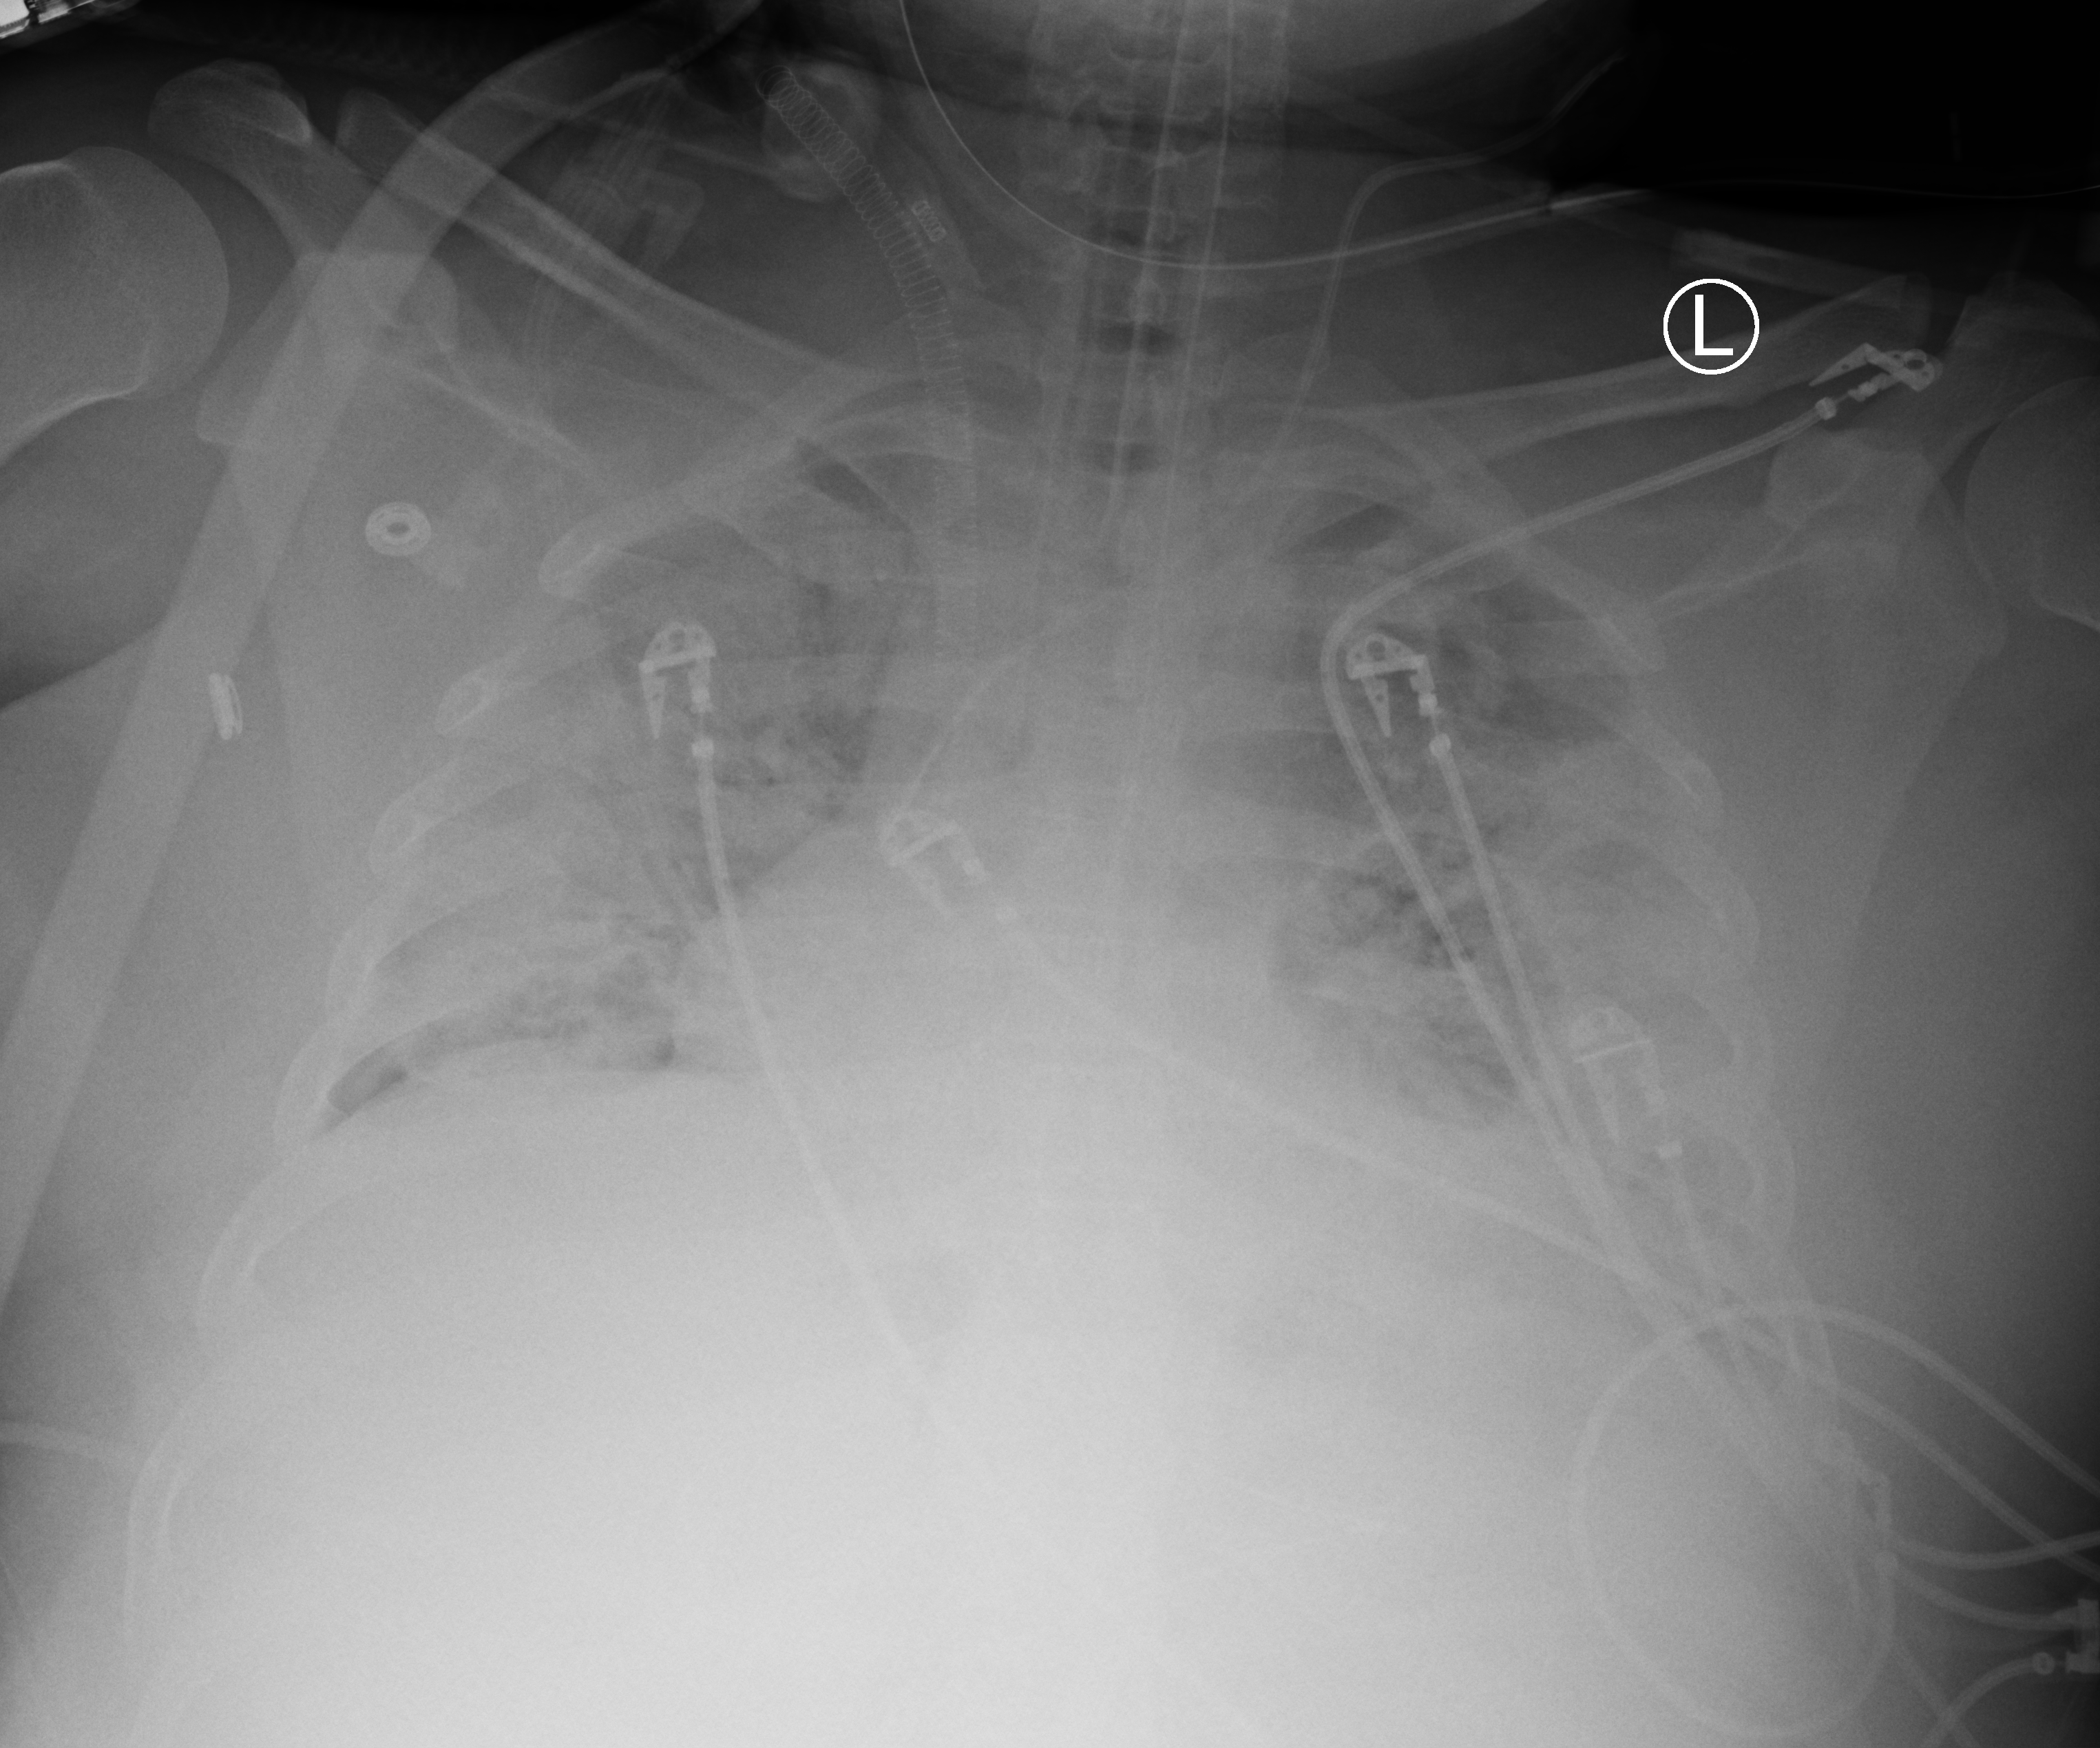
Chest X-ray (portable), anteroposterior (AP) projection. Adult patient hospitalised with COVID-19, age 18–59 years.
Admission-level facts for this patient (not findings on this image; timing relative to this image not recorded):
- admitted to intensive care during this hospital stay: yes